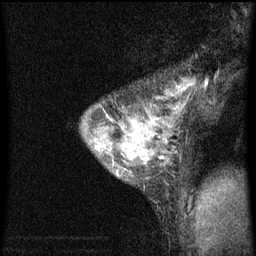
Breast MRI (dynamic contrast-enhanced), one sagittal slice. Position 49 of 60 along the scan axis. Dynamic contrast-enhanced series, image 2 of 3 at this slice position (ordered by acquisition). 1.5 T. TE 4.2 ms, TR 8 ms. 256 × 256 image matrix, field of view 180 × 180 mm. Patient: female, 33 years.
Structures marked on this image (semi-automatic segmentation, software-assisted and operator-edited):
- analysis volume of interest (the breast-tissue region the enhancement analysis was run in; not a lesion): bounding box [x1, y1, x2, y2] px = [81, 82, 197, 215]
- tumour enhancement mask (voxels above the 70 % enhancement threshold inside the analysis volume of interest): [97, 106, 178, 175]